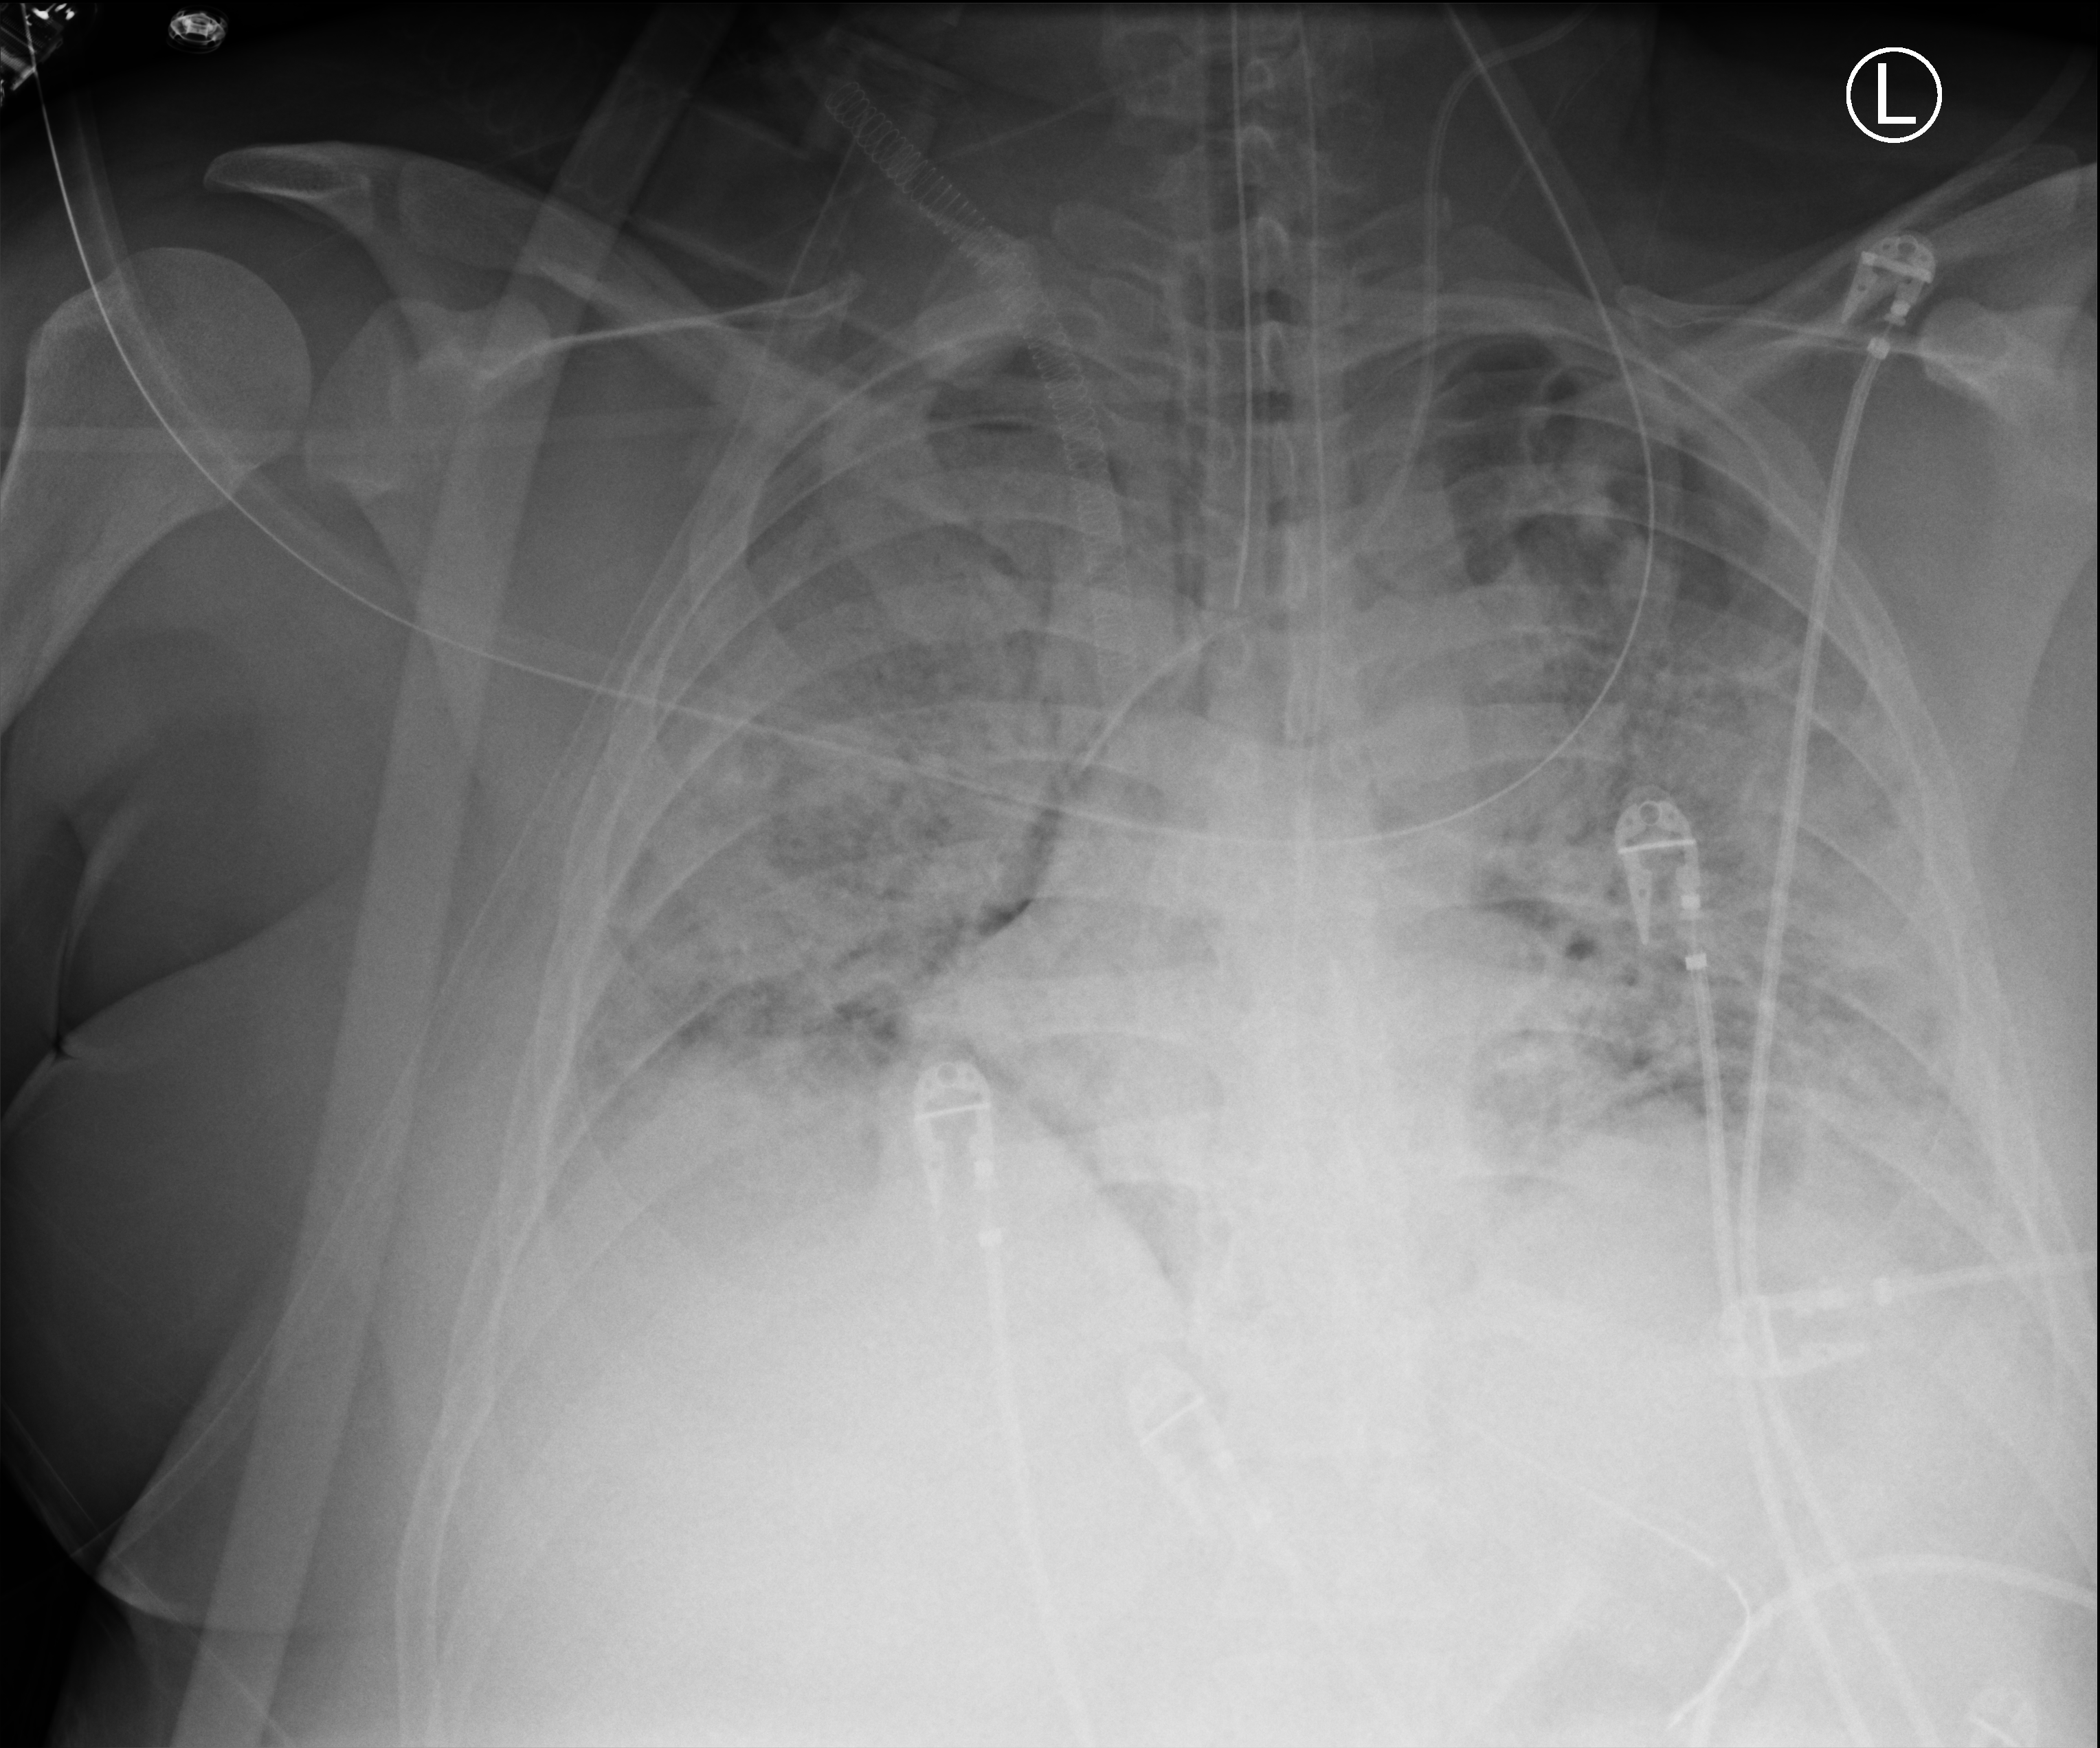
Portable chest radiograph; anteroposterior (AP) projection. Patient hospitalised with COVID-19, aged 18–59 years.
Admission-level facts for this patient (not findings on this image; timing relative to this image not recorded):
- mechanically ventilated during this hospital stay: yes
- other chronic lung disease (admission record): no
- admitted to intensive care during this hospital stay: yes